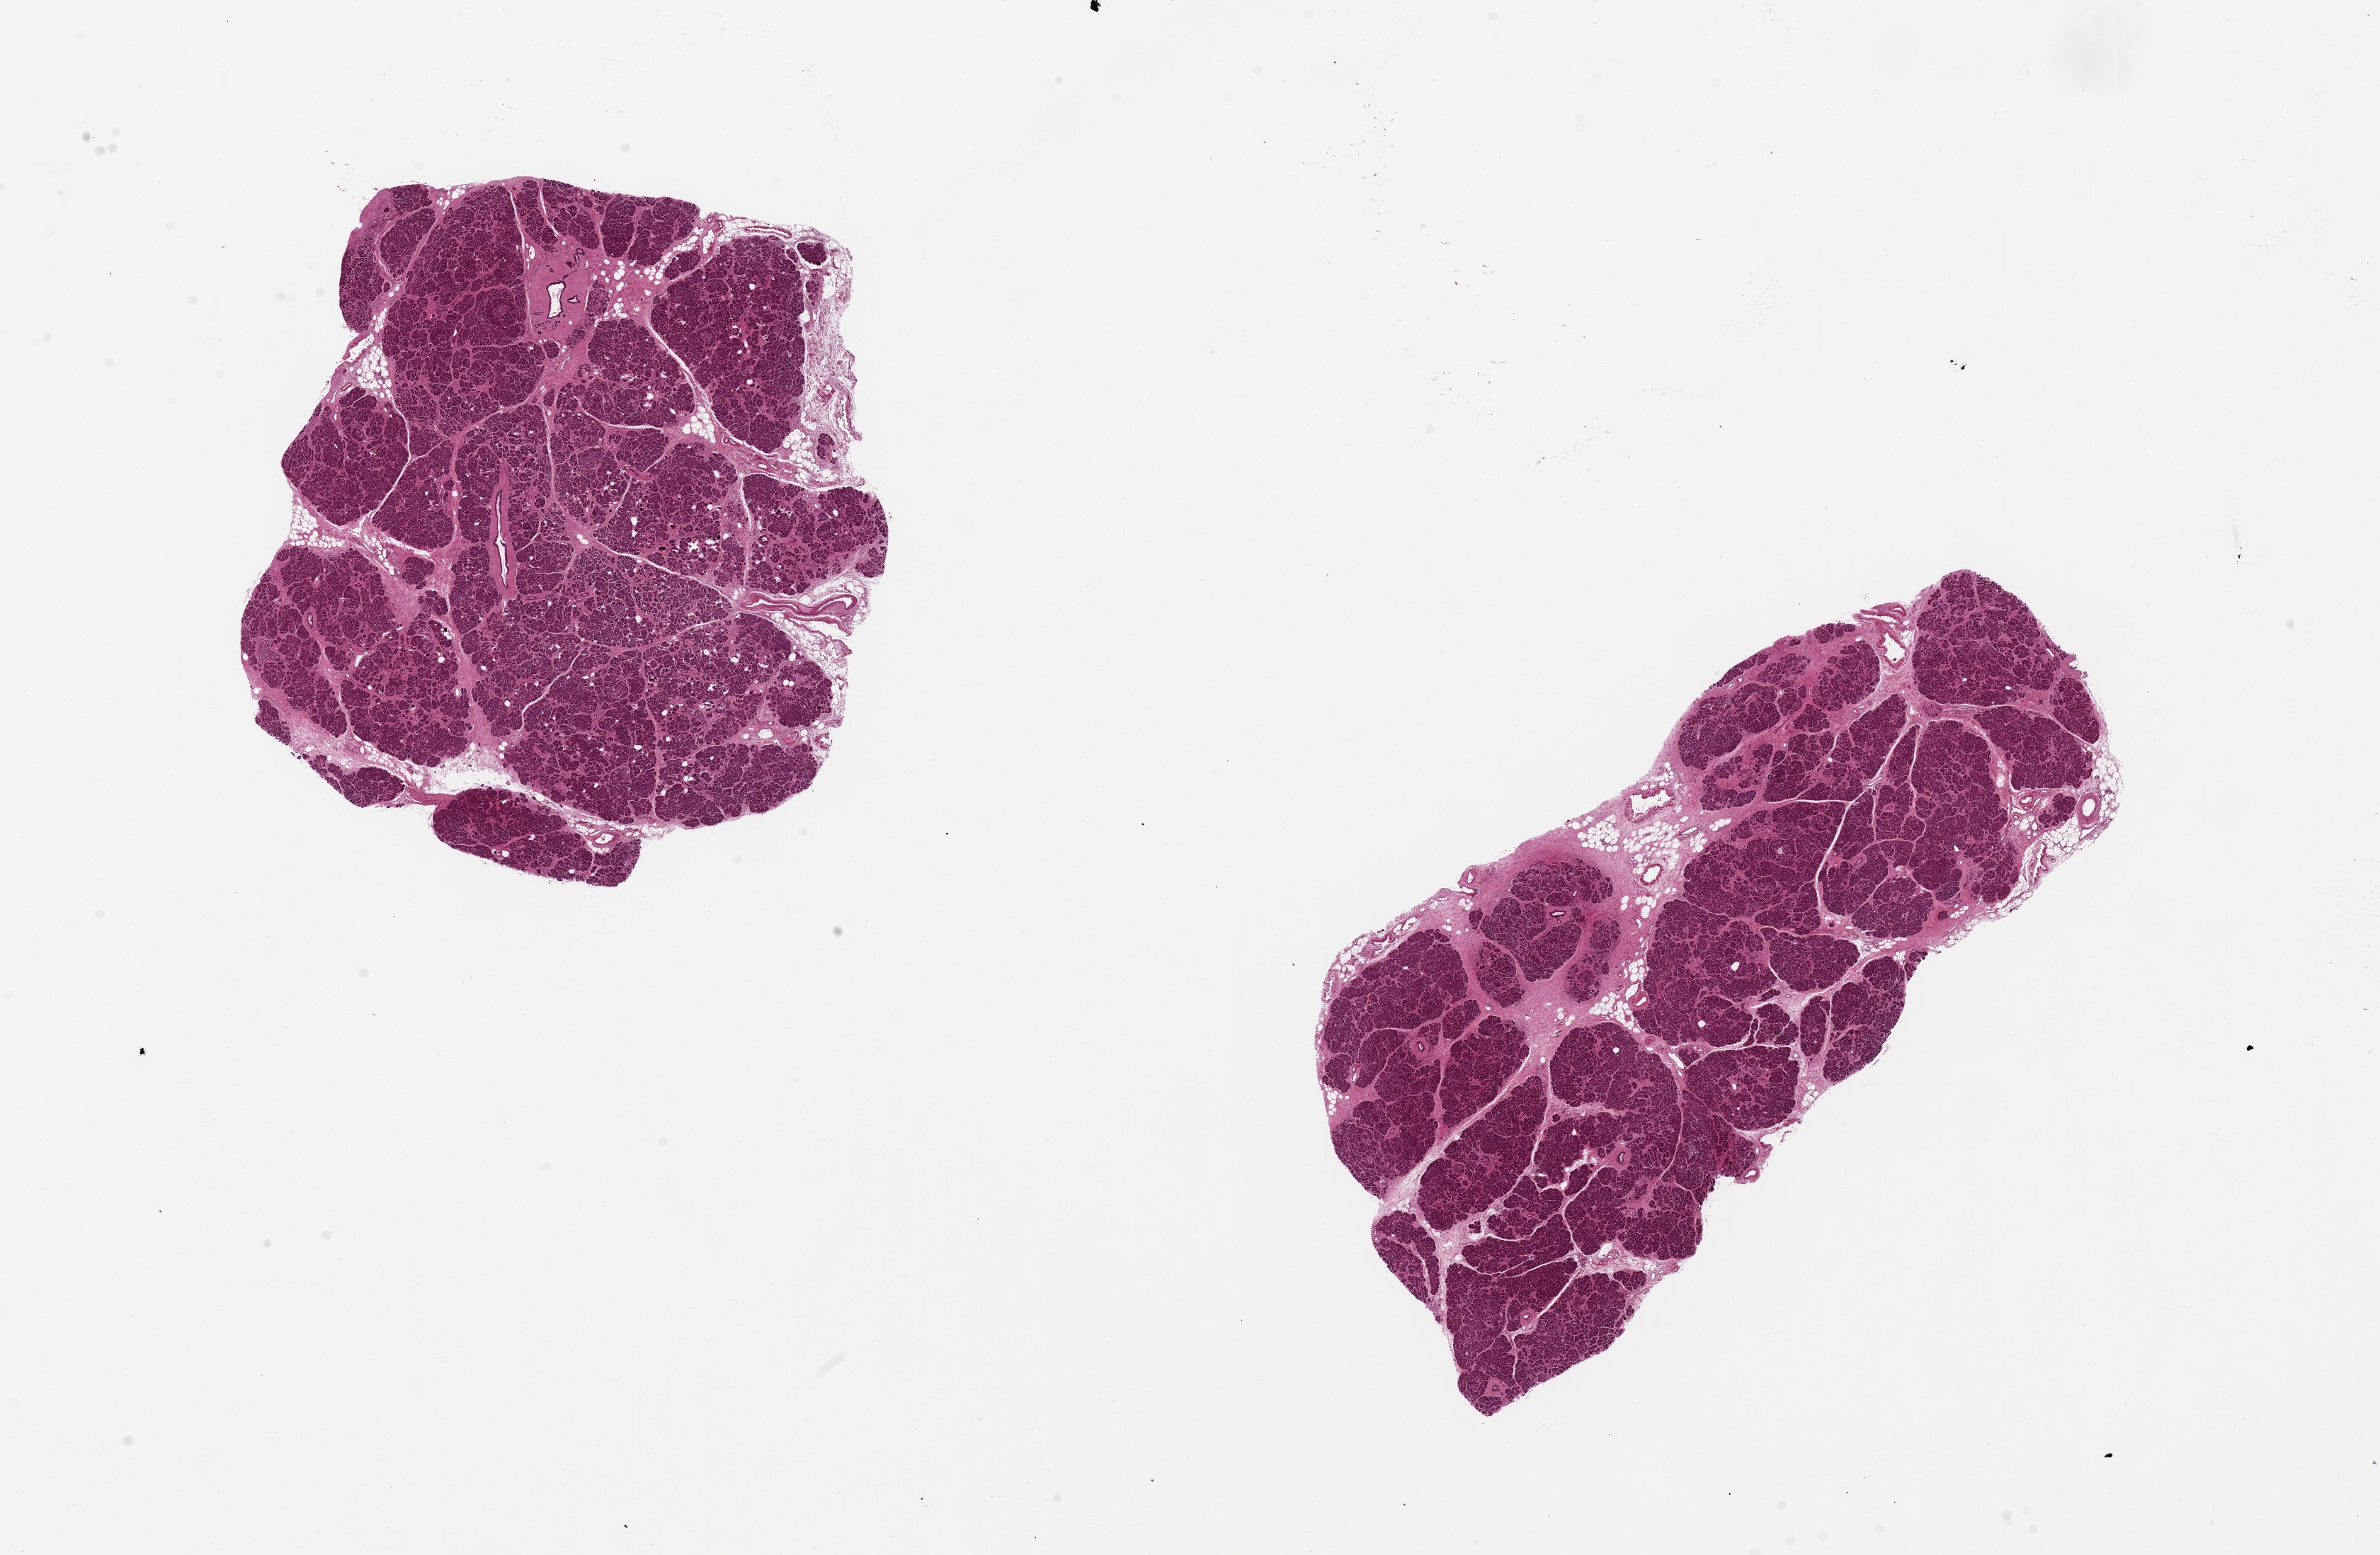
Whole-slide image, hematoxylin and eosin (H&E) stain, a low-resolution overview of the entire scanned area, about 26.6 x 17.4 mm; PAXgene-fixed paraffin-embedded (PFPE) section; section of pancreas (target tissue); tissue donor sample. Female donor.
Review note (as recorded): 2 pieces, 8x7 & 11x5mm; mild-moderate interstitial fibrosis.